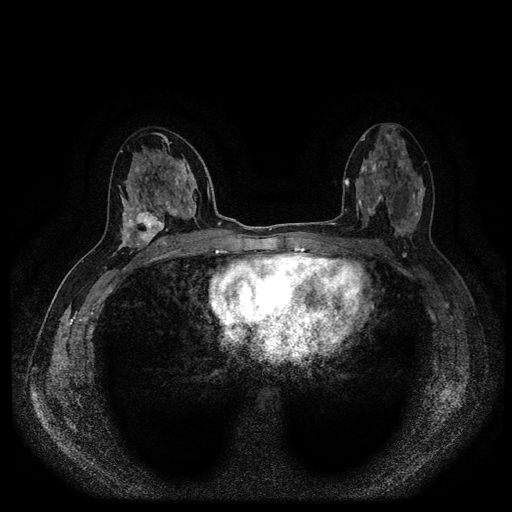
Breast MRI (dynamic contrast-enhanced, multi-phase), one axial slice. Position 52 of 116 along the scan axis. Dynamic contrast-enhanced series, time point 2 of 5 at this slice position (early post-contrast). 1.5 T. TE 2.6 ms, TR 5.4 ms. 2 mm slice thickness. 512 × 512 image matrix. Patient: female, 48 years.
Annotated regions visible in this slice (semi-automatic segmentation, software-assisted and operator-edited):
- breast lesion (labelled 'tumour' in the annotation; benign lesions carry a separate 'benign' label): bounding box (x1, y1, x2, y2) in pixels: (135, 207, 165, 247)